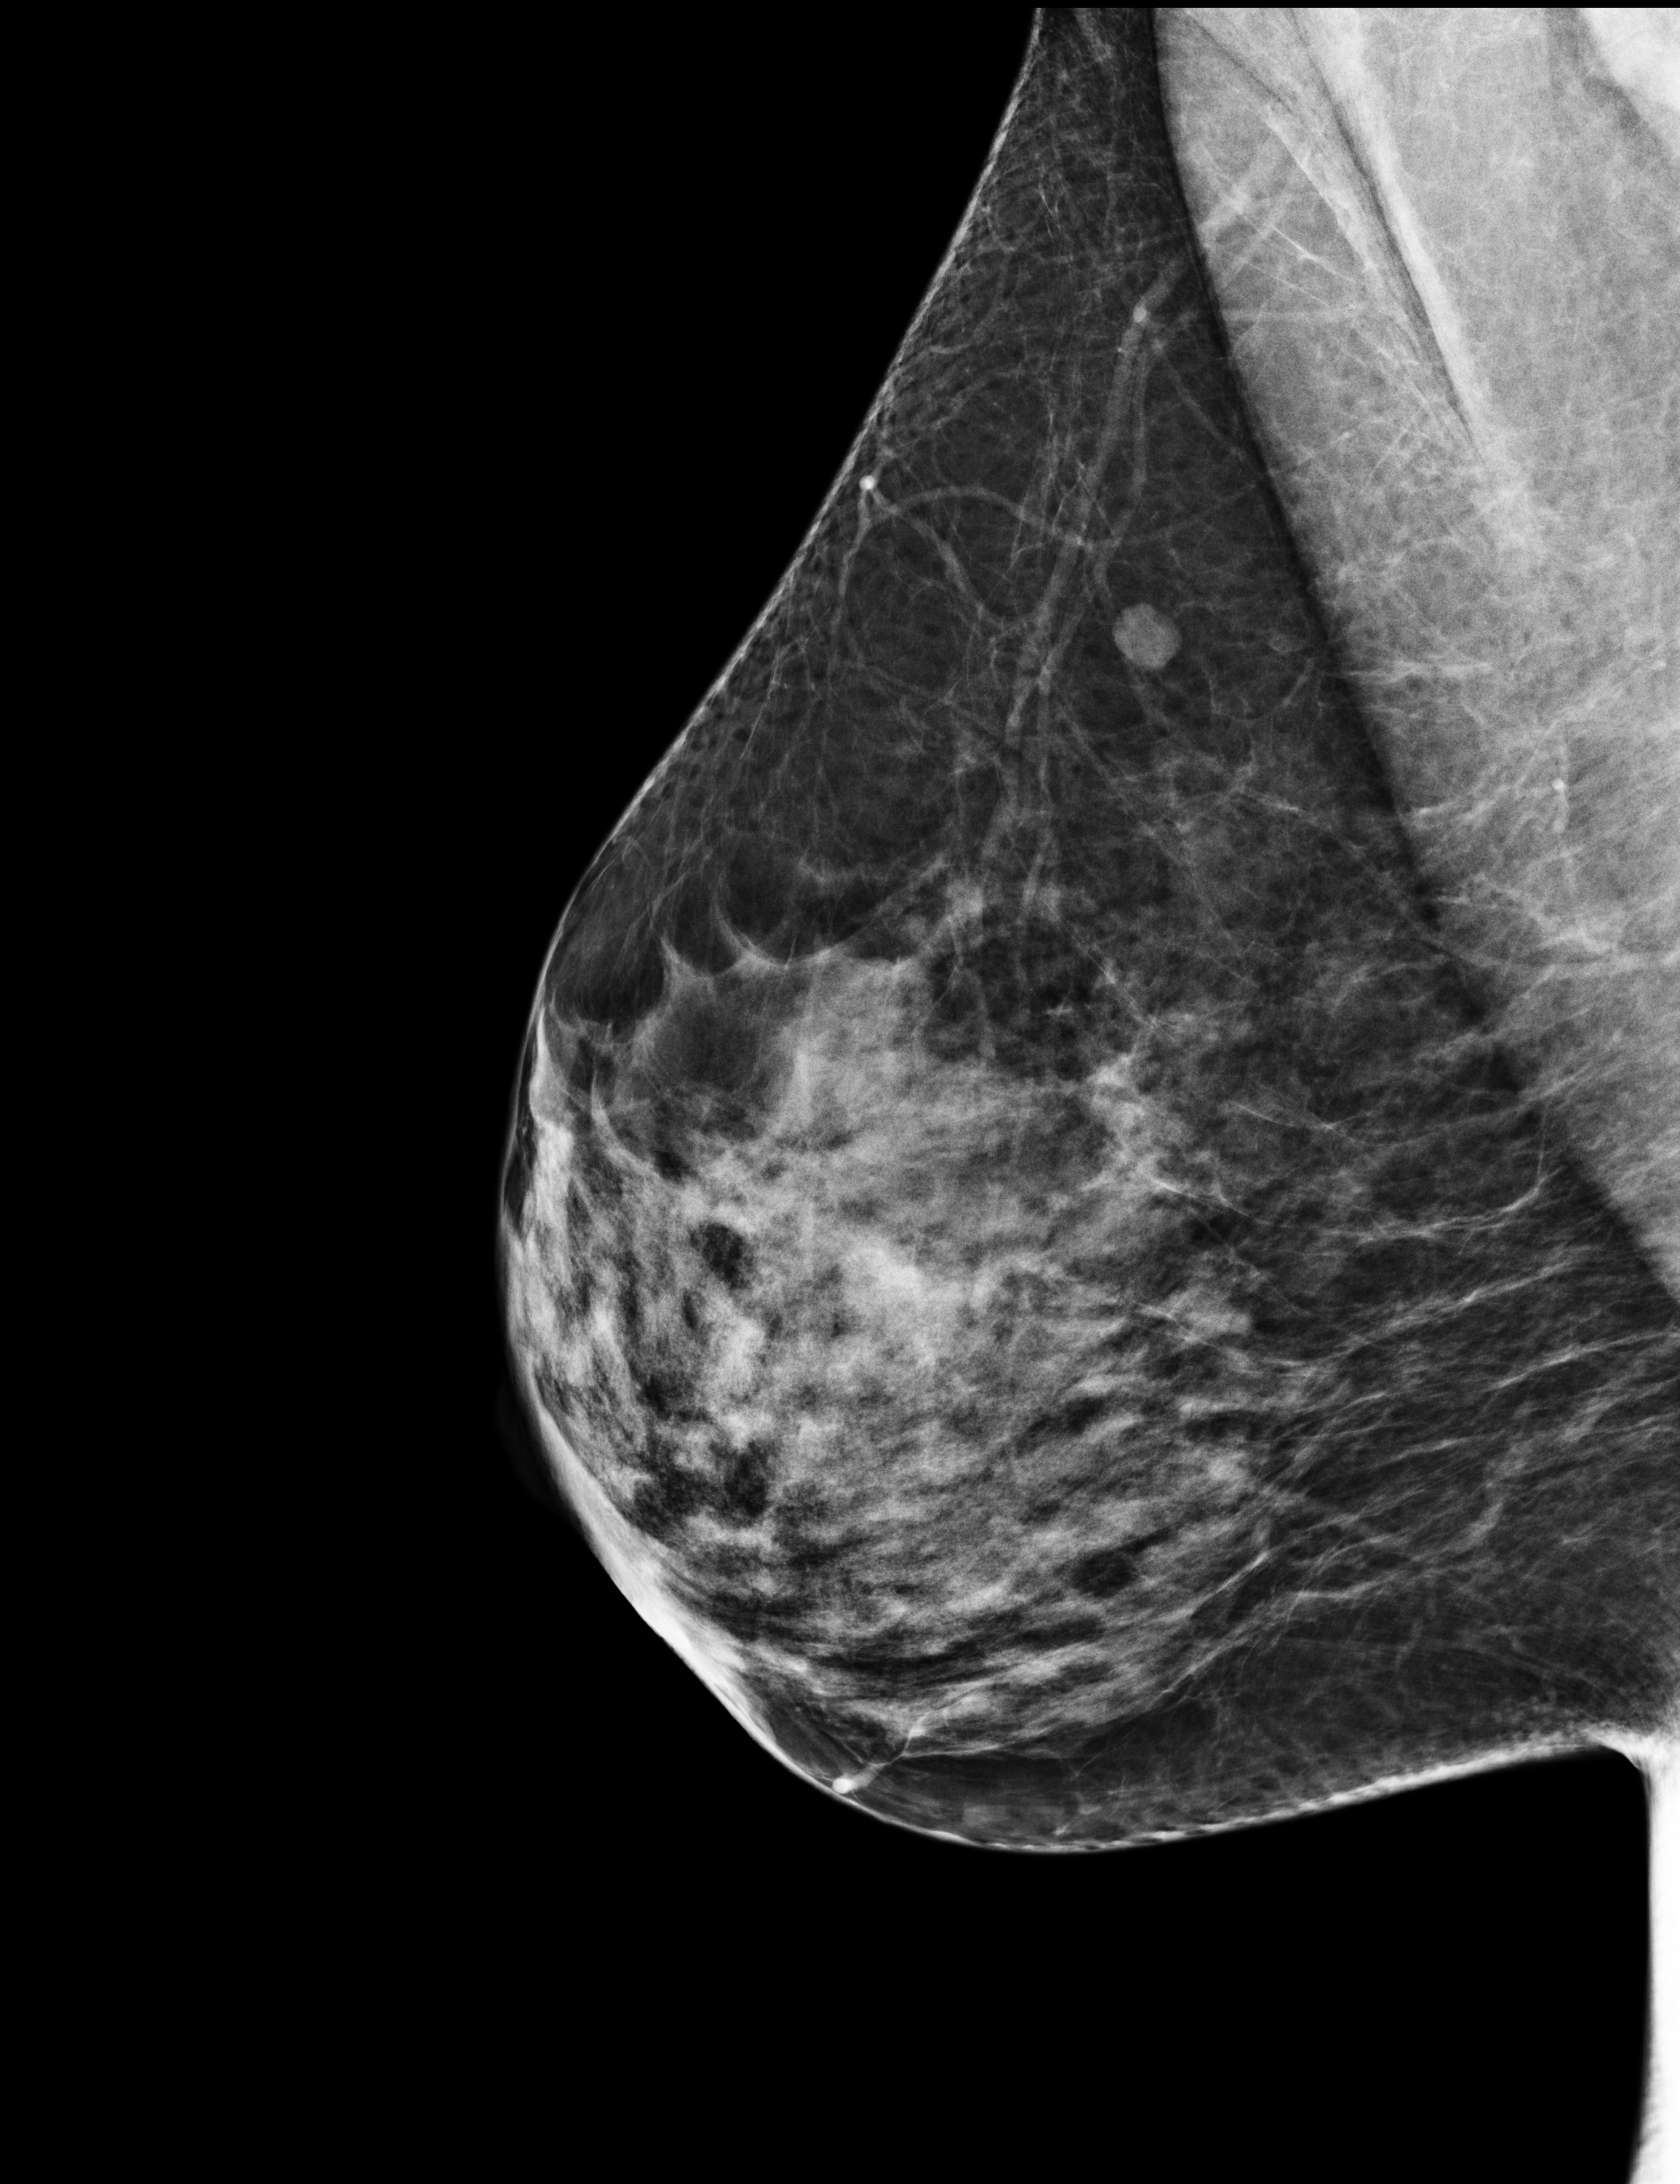
Screening examination. Patient aged 54 years (female).
Image type: full-field digital mammogram. Breast: right. Projection: MLO view.